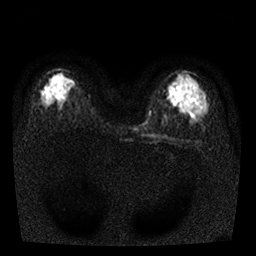
Breast MRI, one axial slice. Position 15 of 25 along the scan axis. Diffusion-weighted series; image 2 of 4 stored at this slice position (different b-values; order by instance number). 1.5 T. 4 mm slice thickness. 256 × 256 image matrix, field of view 310 × 310 mm. Female patient.
Annotated regions visible in this slice (outlined manually by an expert reader):
- tumour on diffusion-weighted imaging: bounding box (x1, y1, x2, y2) in pixels: (45, 92, 49, 96)